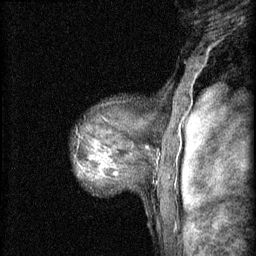
Breast MRI (dynamic contrast-enhanced), one sagittal slice. Position 49 of 60 along the scan axis. 3 images stored at this slice position (order not interpretable as contrast timing). 1.5 T. TE 4.2 ms, TR 8.2 ms. 256 × 256 image matrix, field of view 180 × 180 mm. Patient: female, 48 years.
Structures marked on this image (semi-automatic segmentation, software-assisted and operator-edited):
- analysis volume of interest (the breast-tissue region the enhancement analysis was run in; not a lesion): bounding box <84,138,133,183> (left, top, right, bottom; pixels)
- tumour enhancement mask (voxels above the 70 % enhancement threshold inside the analysis volume of interest): <102,164,117,175>